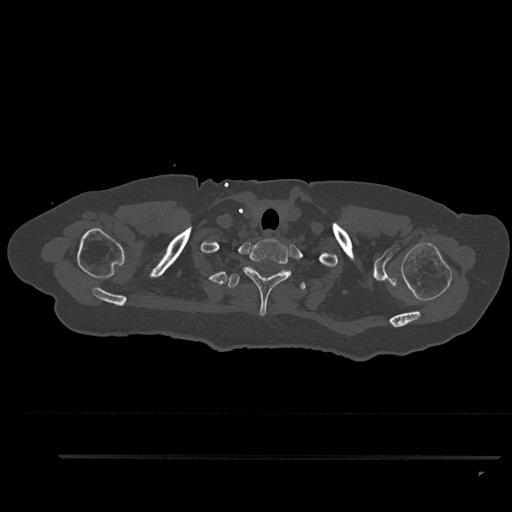
CT including the spine, one axial slice. Position 754 of 797 along the scan axis. 120 kVp. Bone window (W 1800 / L 400 HU). 512 × 512 image matrix, field of view 408 × 408 mm. Patient: female, 44 years. From the clinical record (not read from this slice): primary cancer: renal.
Structures marked on this image (semi-automatically segmented with operator editing):
- T1 vertebra: bounding box <243,238,292,316> (left, top, right, bottom; pixels)
- T2 vertebra: <228,273,306,290>